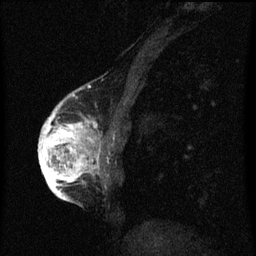
Breast MRI (dynamic contrast-enhanced), one sagittal slice. Position 20 of 60 along the scan axis. Dynamic contrast-enhanced series, image 2 of 3 at this slice position (ordered by acquisition). 1.5 T. TE 4.2 ms, TR 8 ms. 2 mm slice thickness. 256 × 256 image matrix. Female patient, age 56 years.
Outlined on this slice (semi-automatically segmented with operator editing):
- analysis volume of interest (the breast-tissue region the enhancement analysis was run in; not a lesion): box from (x=42, y=110) to (x=103, y=193) px
- tumour enhancement mask (voxels above the 70 % enhancement threshold inside the analysis volume of interest): (x=42, y=110)–(x=99, y=193)